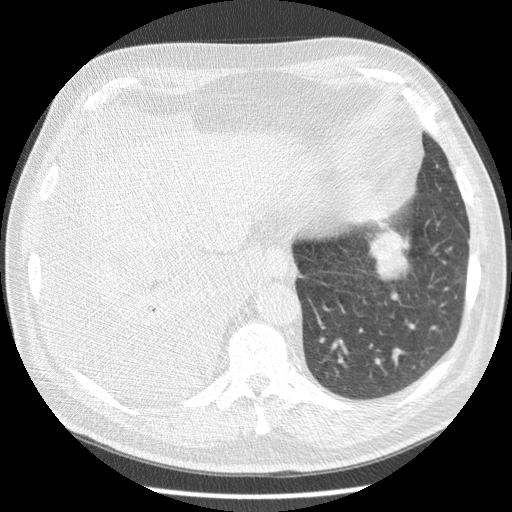
Axial slice from a low-dose chest CT screening exam. Third annual screen. Lung window (W 1500 / L -600 HU). 2.5 mm slice thickness. Slice 52 of 180 in the series. Male, age 63 years at enrolment. Current smoker at enrolment.
Expert-annotated lung lesion, bounding box [x1, y1, x2, y2] px = [358, 217, 421, 281]. The exam's reader record, not a measurement of the box and not confirmed to be the same lesion: non-calcified nodule or mass ≥4 mm, left lower lobe, 34 × 31 mm, smooth margins, soft tissue attenuation, pre-existing on the prior screen: yes; interval growth: yes. Lung cancer was diagnosed 30 days after this screen: squamous cell carcinoma, NOS, left lower lobe, stage IB (AJCC 6th edition), 48 mm at pathology.